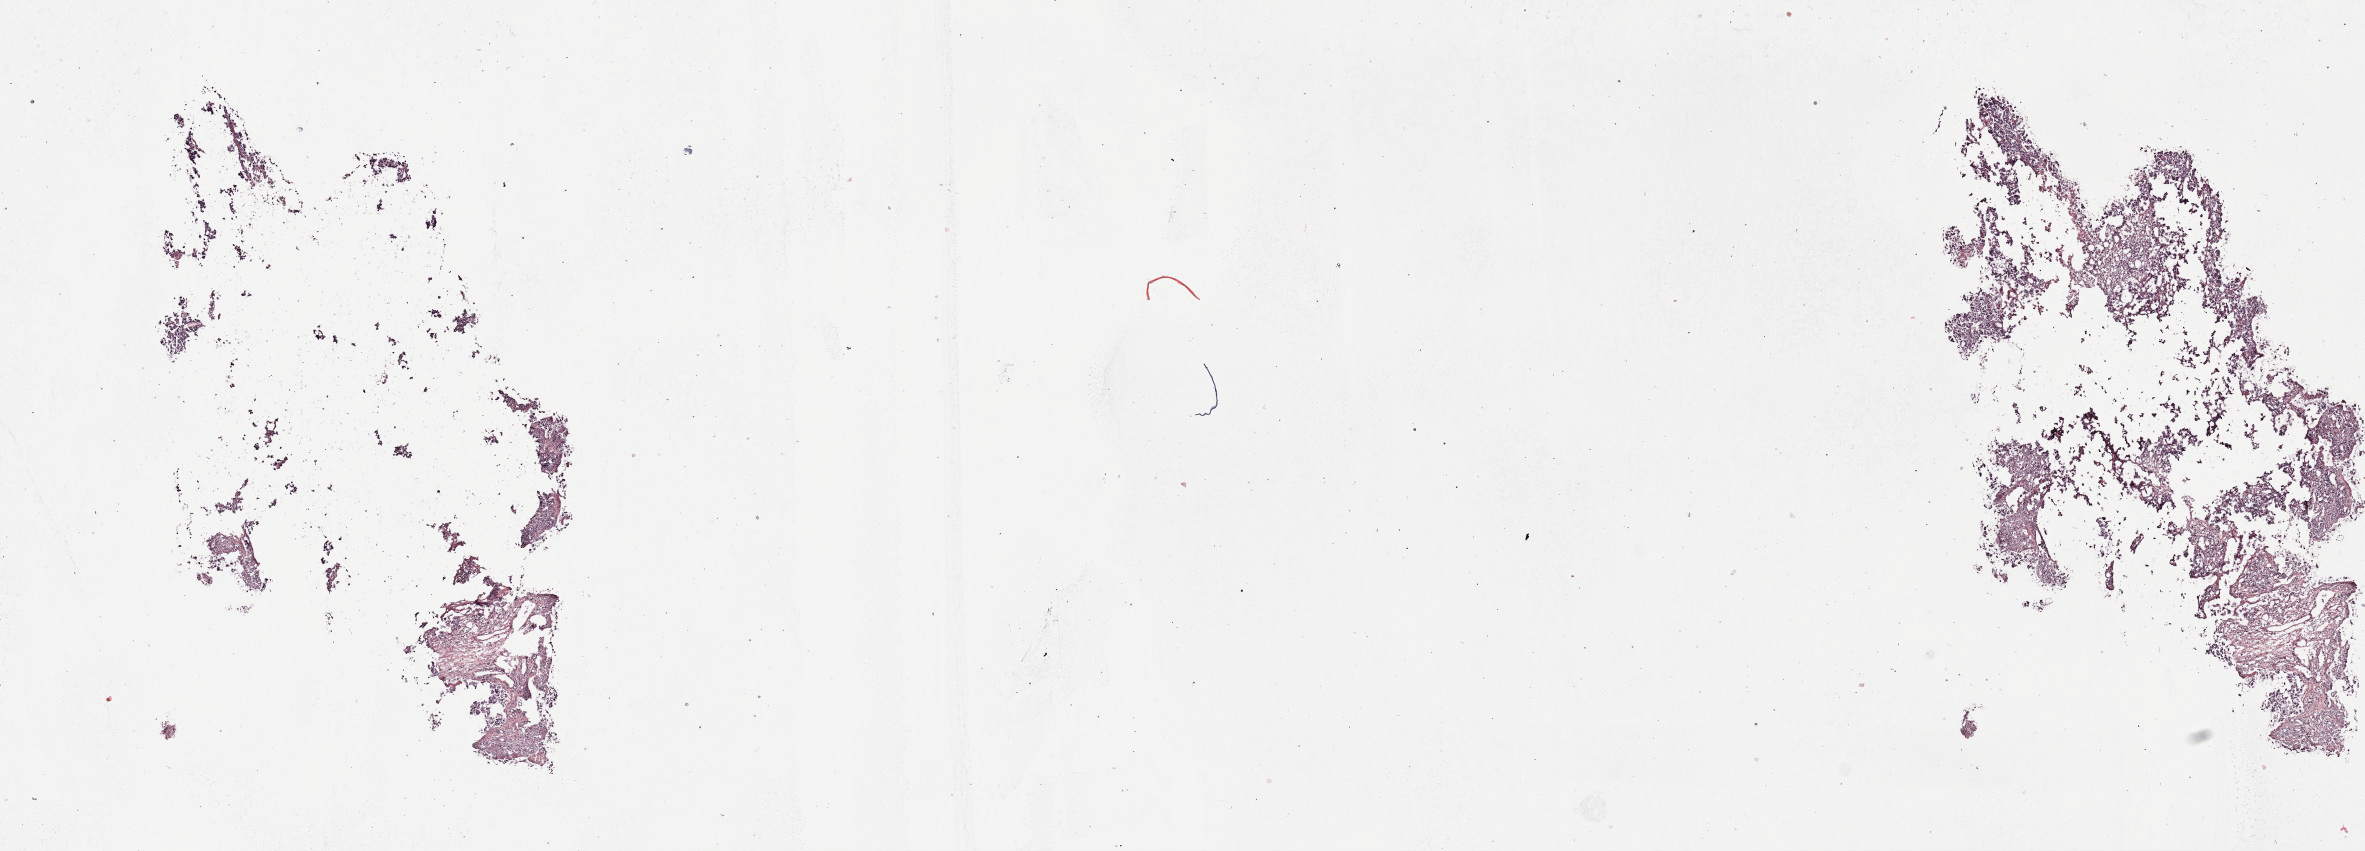
H&E whole-slide image, a low-resolution overview of the entire scanned area, about 19.1 x 6.9 mm, frozen section, metastatic tumour sample, sampled site not recorded. Male patient; age at initial diagnosis 71 years. Slide review estimates, as recorded: tumour cells 65%, tumour nuclei 65%, normal cells 0%, stromal cells 30%, necrosis 5%. Inflammatory infiltration, as recorded: lymphocyte infiltration 3%, monocyte infiltration 2%, neutrophil infiltration 3%.
This section: metastatic tumour tissue. Patient diagnosis: Malignant melanoma, NOS.